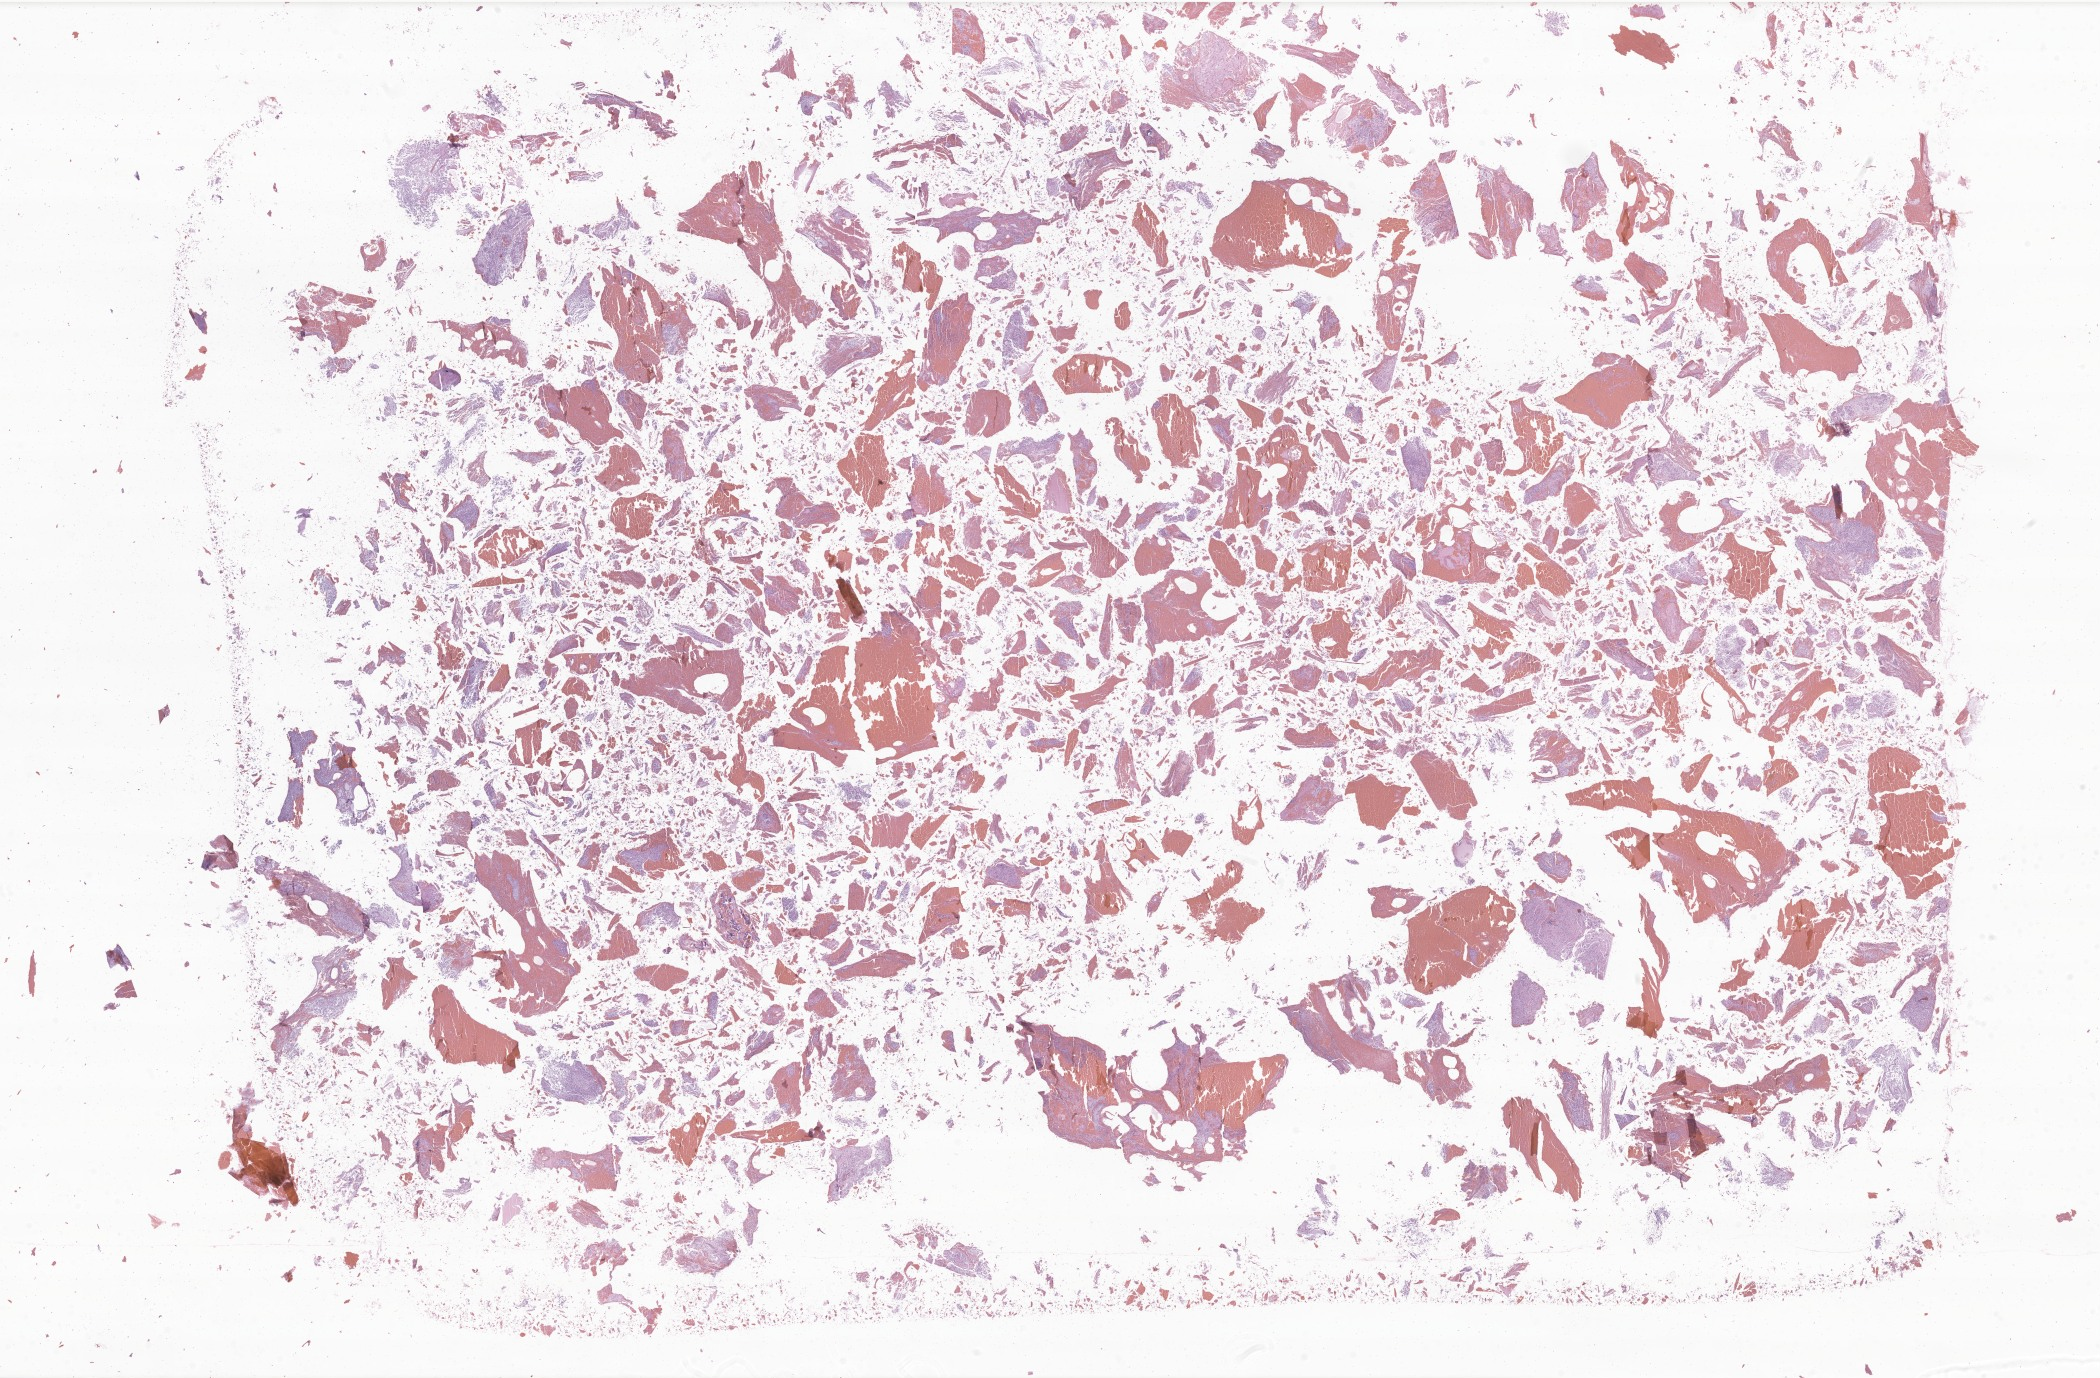
Whole-slide image, hematoxylin and eosin (H&E) stain of tumor tissue from the brain, shown as a low-resolution overview of the whole scanned area (about 35.4 x 23.2 mm). Formalin-fixed, paraffin-embedded (FFPE) tissue. Female patient, age 402 days (about 1.1 years).
- recorded diagnosis: Pilocytic astrocytoma